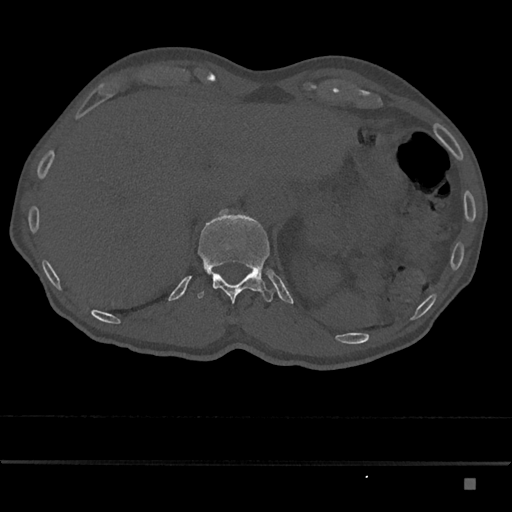
CT including the spine, one axial slice. Slice 612 of 797 in the series (ordered by position). 120 kVp. Bone window (W 1800 / L 400 HU). 0.5 mm slice thickness. 512 × 512 image matrix, field of view 390 × 390 mm. Male patient, age 72 years. From the clinical record (not read from this slice): primary cancer: prostate.
Structures marked on this image (semi-automatic segmentation, software-assisted and operator-edited):
- T12 vertebra: bounding box <197,213,275,303> (left, top, right, bottom; pixels)